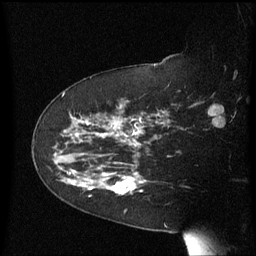
Breast MRI (dynamic contrast-enhanced), one sagittal slice; slice 41 of 60 in the series (ordered by position); dynamic contrast-enhanced series, image 2 of 3 at this slice position (ordered by acquisition); 1.5 T; TE 4.2 ms, TR 8.4 ms; 256 × 256 image matrix. Patient: female, 63 years. From the clinical record (not read from this slice): setting: breast cancer imaged before/during neoadjuvant chemotherapy; receptor status: HER2-positive.
Structures marked on this image (semi-automatic segmentation, software-assisted and operator-edited):
- analysis volume of interest (the breast-tissue region the enhancement analysis was run in; not a lesion): box from (x=63, y=144) to (x=147, y=206) px
- tumour enhancement mask (voxels above the 70 % enhancement threshold inside the analysis volume of interest): (x=63, y=144)–(x=144, y=194)